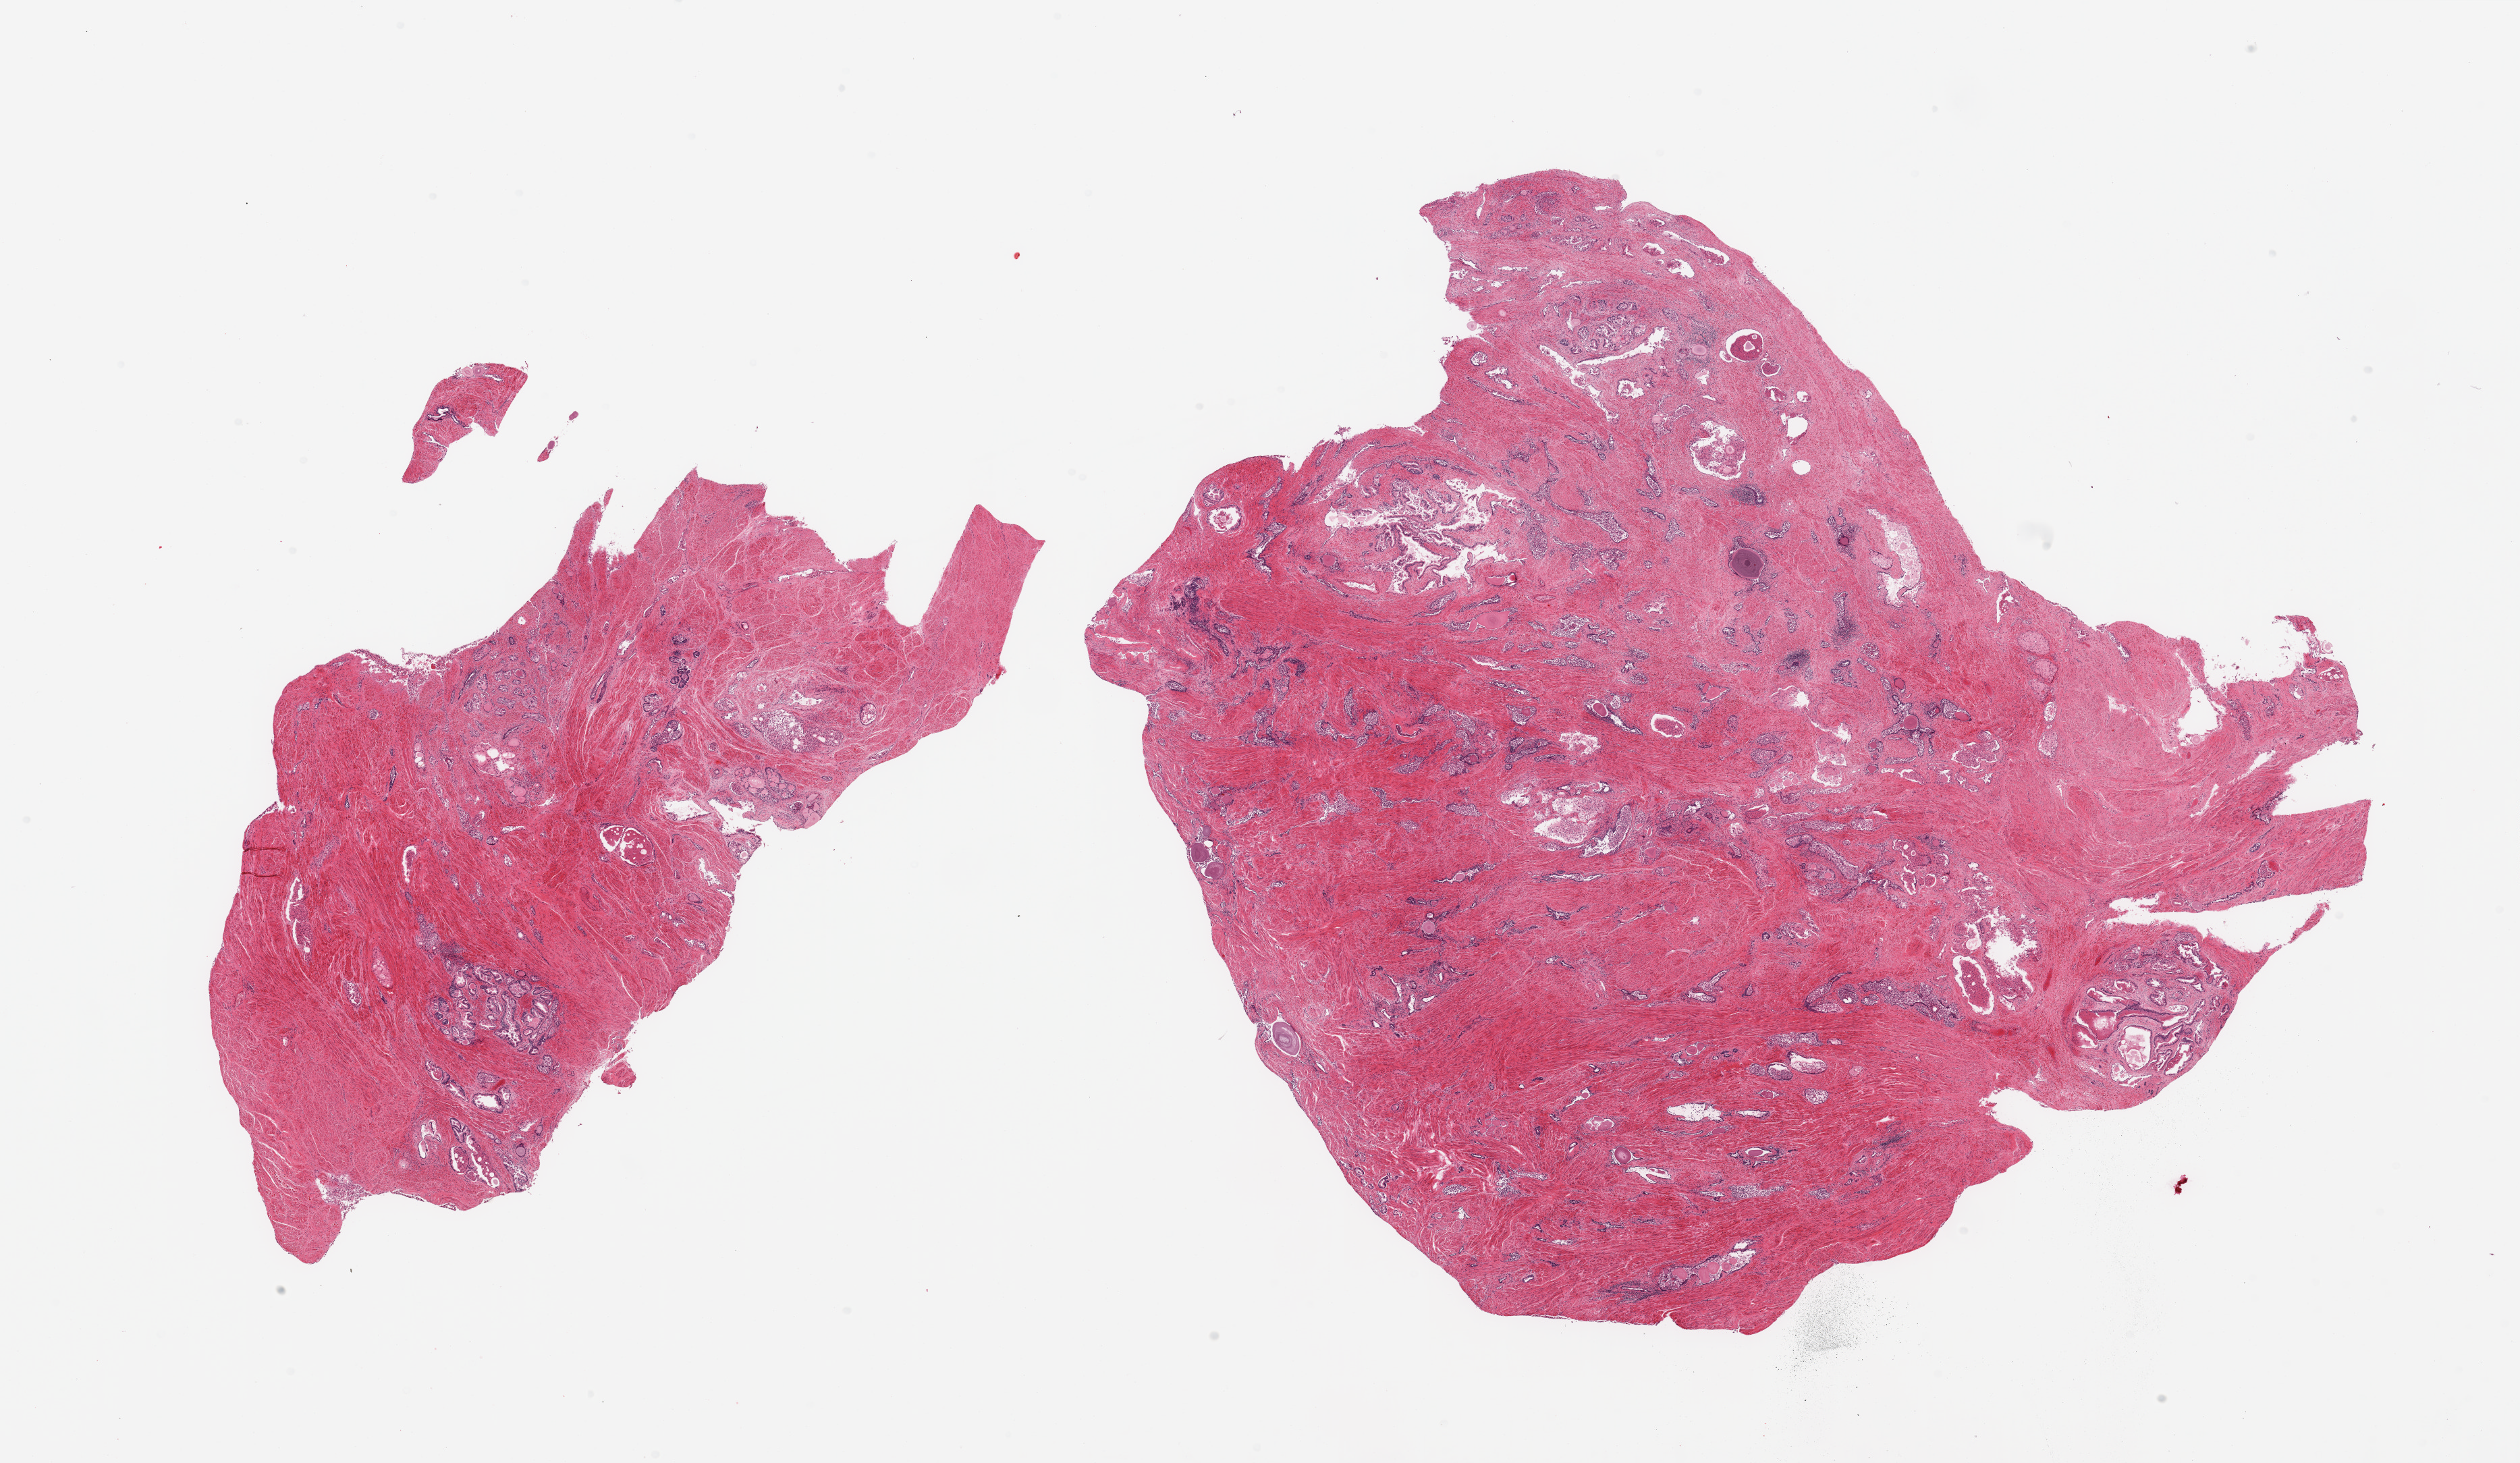
Hematoxylin and eosin (H&E) whole-slide image, a low-resolution overview of the entire scanned area, about 29.5 x 17.1 mm (from a 20x scan); PAXgene-fixed paraffin-embedded (PFPE) section; section of prostate (target tissue); donor tissue sample. Donor sex: male.
Pathologist's review note for this sample: 2 pieces; glands with largely sloughed epithelium, stroma, and few patches of chronic inflammation.